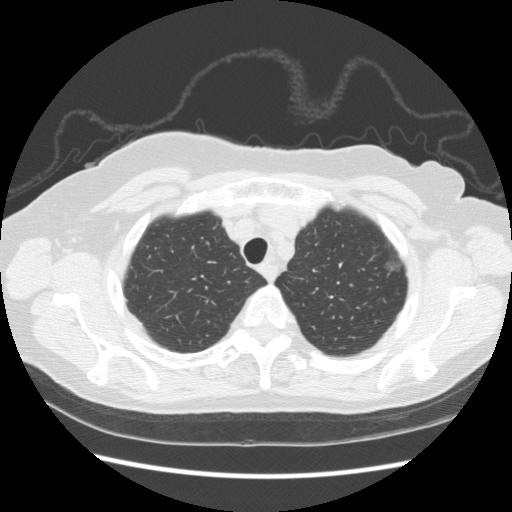
Chest CT (low-dose screening protocol), one axial image; baseline annual screen; lung window (W 1500 / L -600 HU); 2.5 mm slice thickness; standard (soft-tissue) reconstruction kernel (STANDARD); slice 31 of 247 in the series. Female participant, aged 73 years at enrolment. Former smoker at enrolment.
Expert-annotated lung lesion, bounding box [x1, y1, x2, y2] px = [371, 232, 412, 280]. The screening reader recorded 3 non-calcified nodules or masses ≥4 mm on this exam (left upper lobe, left upper lobe, left upper lobe); which of them this box marks is not recorded. Lung cancer was diagnosed 445 days after this screen: bronchiolo-alveolar adenocarcinoma, NOS, left upper lobe, well differentiated (G1), stage IA (AJCC 6th edition), 10 mm at pathology.